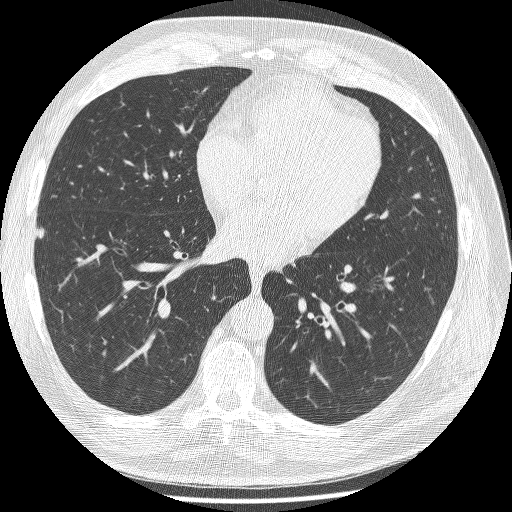
Low-dose screening chest CT, one axial slice. Slice 105 of 241 in the series (ordered by position). Reconstruction kernel BONE. 120 kVp. Lung window (W 1500 / L -600 HU). 512 × 512 image matrix.
Outlined on this slice (manually delineated by an expert):
- lesion 1 (tumor, lower lobe of right lung): bounding box (x1, y1, x2, y2) in pixels: (36, 227, 45, 239)